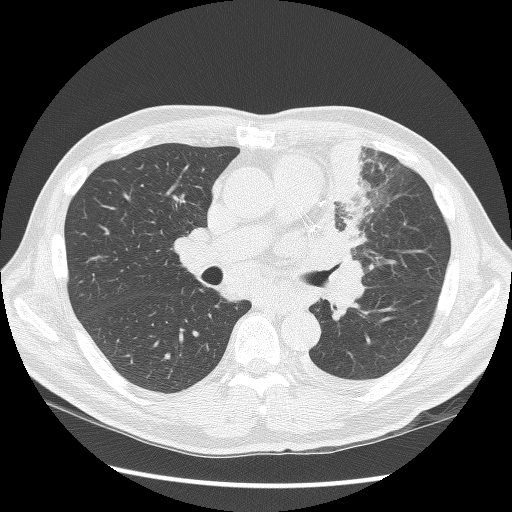
Chest CT (low-dose screening protocol), one axial image; second screening round (one year after baseline); lung window (W 1500 / L -600 HU); lung (sharp) reconstruction kernel (BONE). Male, age 64 years at enrolment. Former smoker at enrolment.
- Lesion marked by an expert reader, bounding box <304,136,390,280> (left, top, right, bottom; pixels).
- Screening reader's record for this exam: no non-calcified nodule ≥4 mm recorded.
- Participant outcome: lung cancer diagnosed 24 days after this screen — small cell carcinoma, NOS, left upper lobe, stage IV (AJCC 6th edition), 100 mm at pathology.